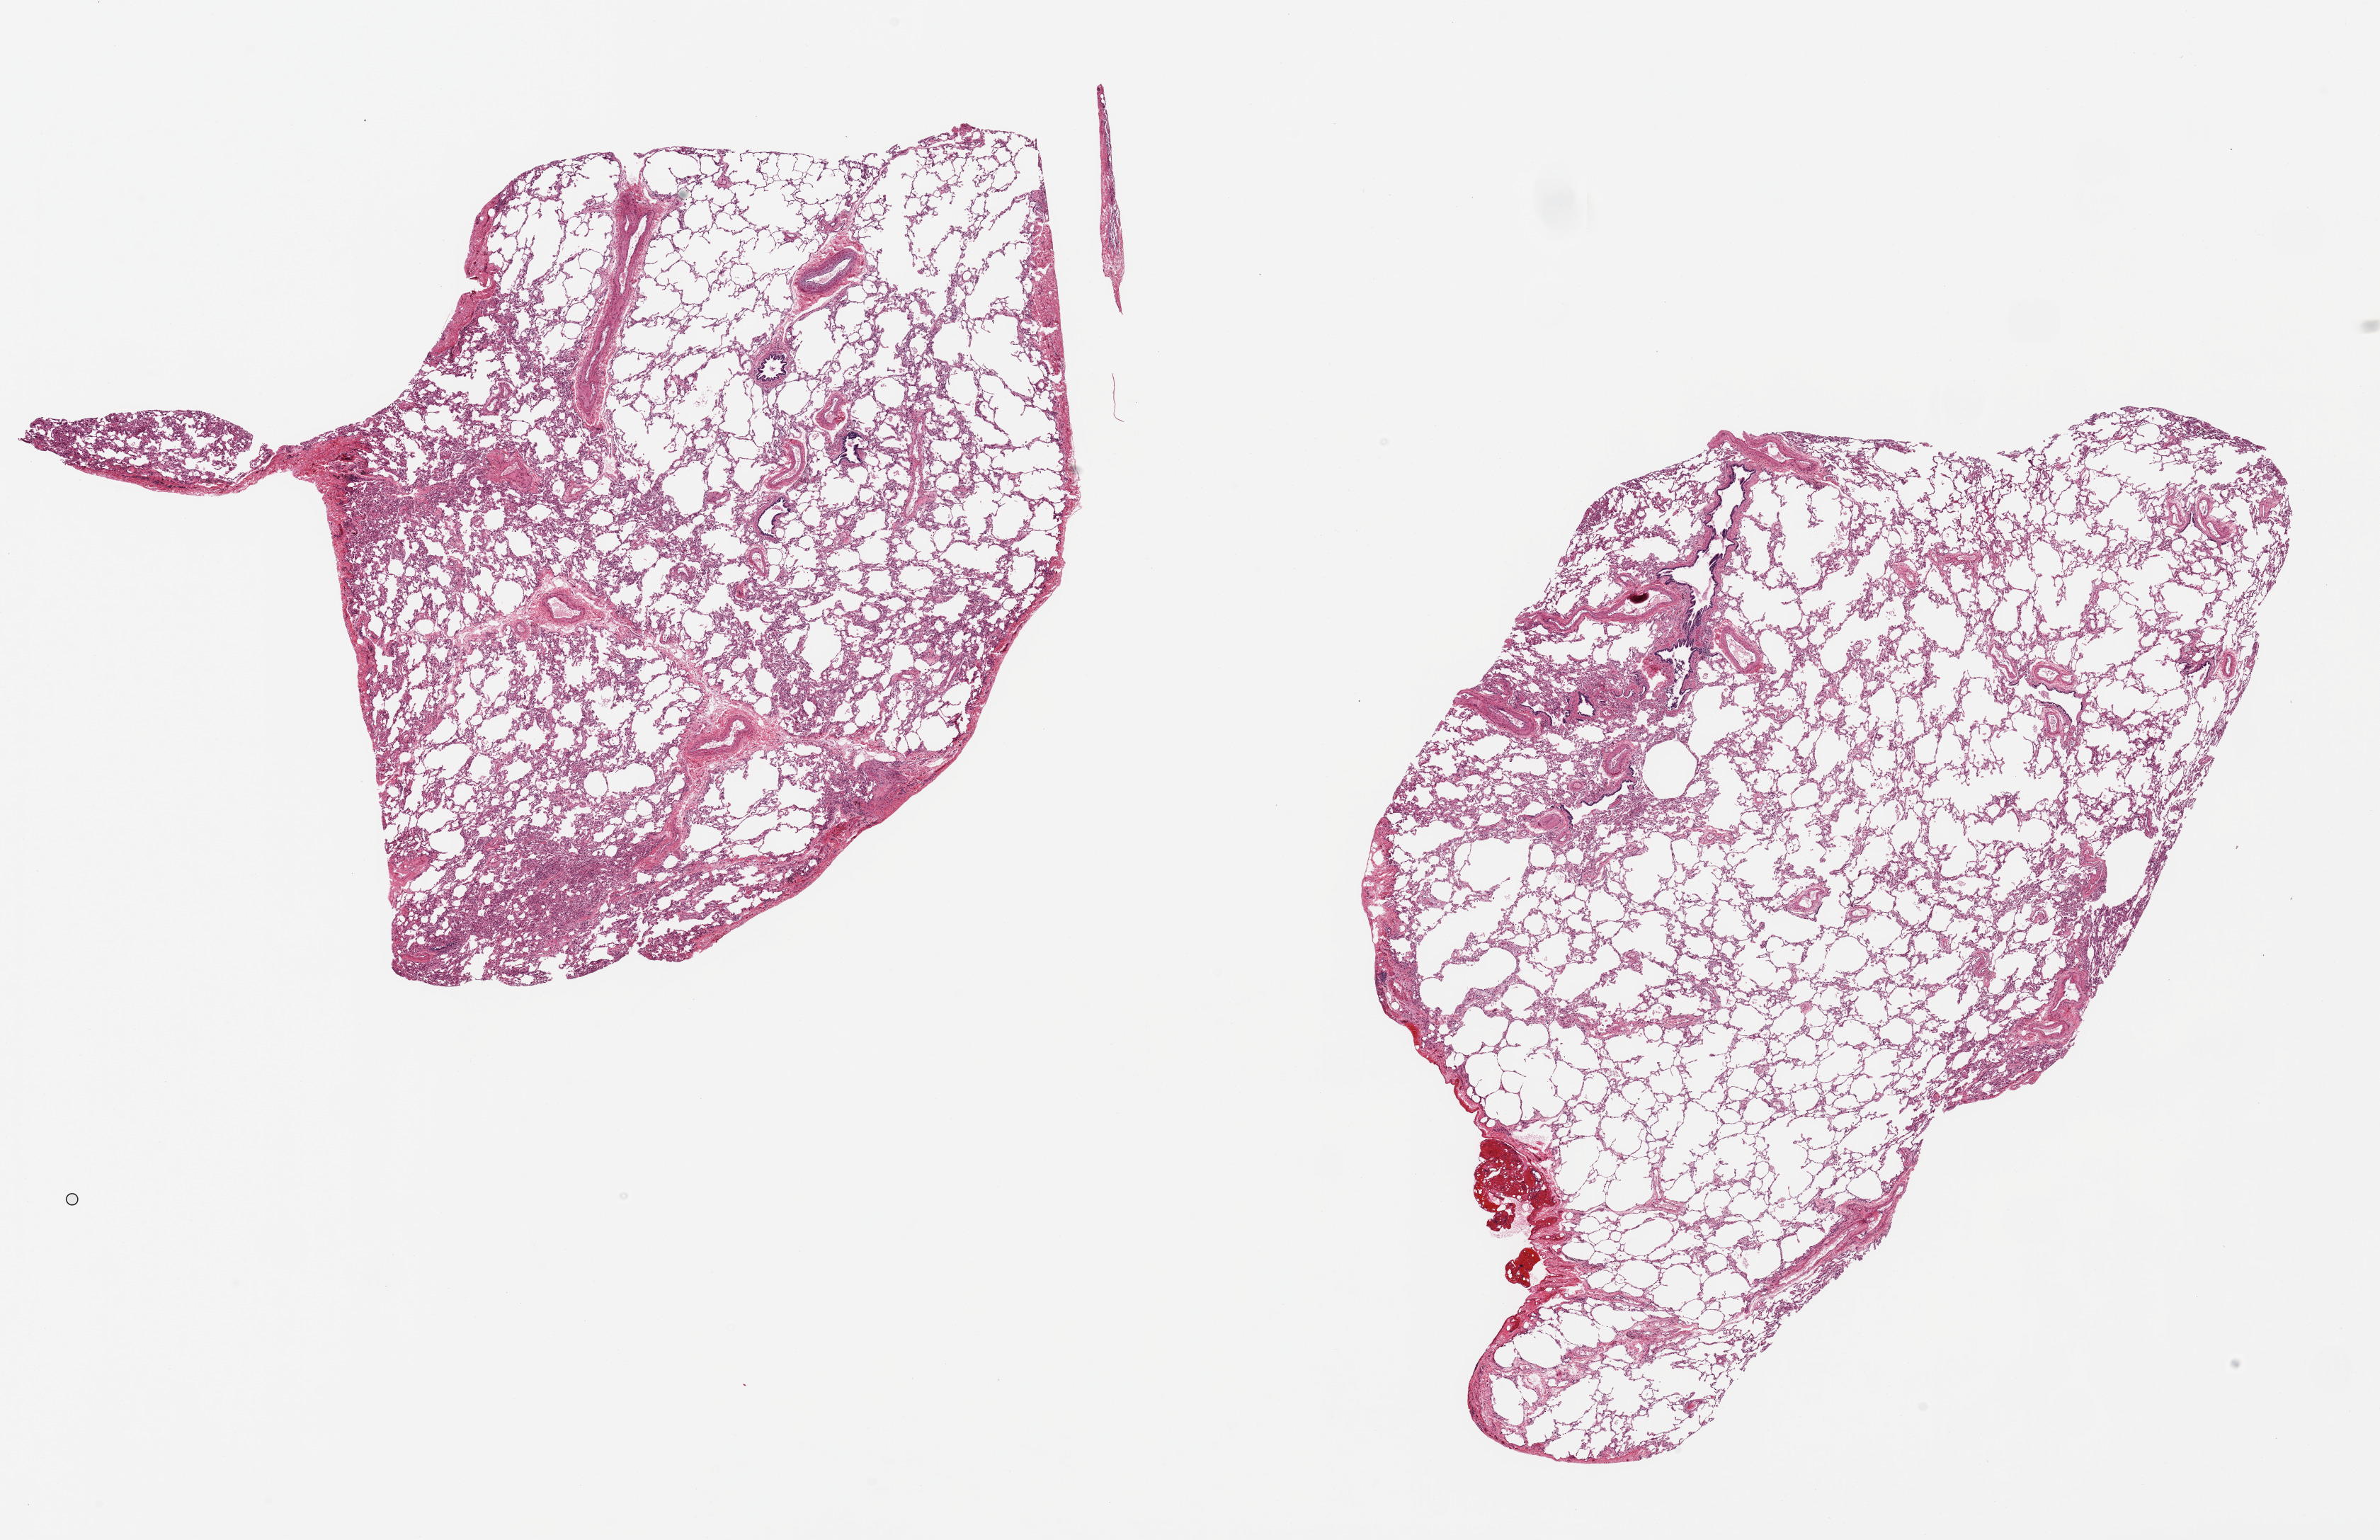
Whole-slide image, H&E stain, brightfield — low-resolution overview of the scanned area, about 26.6 x 17.2 mm (from a 20x scan), PAXgene-fixed, paraffin-embedded tissue, target tissue: lung, donor tissue sample. Donor: male.
• reviewer comment on this tissue sample: 2 ~12x7mm pieces, fairly clean, minimal inflammation, patchy atelectasis